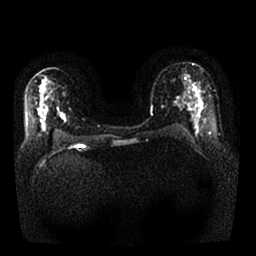
Breast MRI, one axial slice. Position 17 of 25 along the scan axis. Diffusion-weighted series; image 2 of 4 stored at this slice position (different b-values; order by instance number). 1.5 T. 256 × 256 image matrix, field of view 340 × 340 mm. Female patient.
Annotated regions visible in this slice (manually delineated by an expert):
- tumour on diffusion-weighted imaging: bounding box <196,93,201,108> (left, top, right, bottom; pixels)